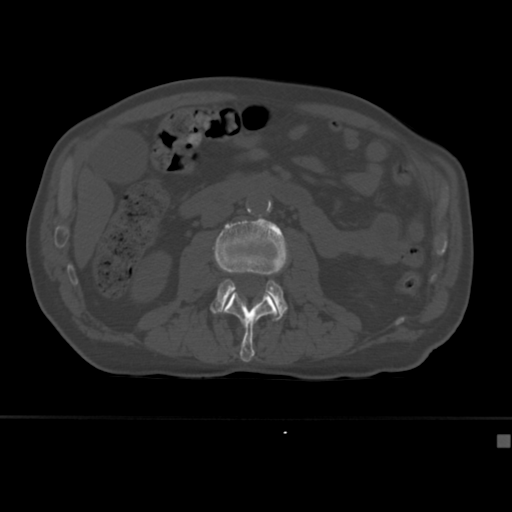
CT including the spine, one axial slice; slice 138 of 430 in the series (ordered by position); reconstruction kernel Br40s; 120 kVp; bone window (W 1800 / L 400 HU); 1.5 mm slice thickness; 512 × 512 image matrix. Male patient, age 64 years. Case-level facts recorded for this patient, not image findings: primary cancer: uterus; vertebrae with lytic lesions (as recorded): T1, T4, T5, T7, L5.
Outlined on this slice (semi-automatically segmented with operator editing):
- L2 vertebra: bounding box (x1, y1, x2, y2) in pixels: (223, 292, 277, 362)
- L3 vertebra: (210, 218, 289, 321)